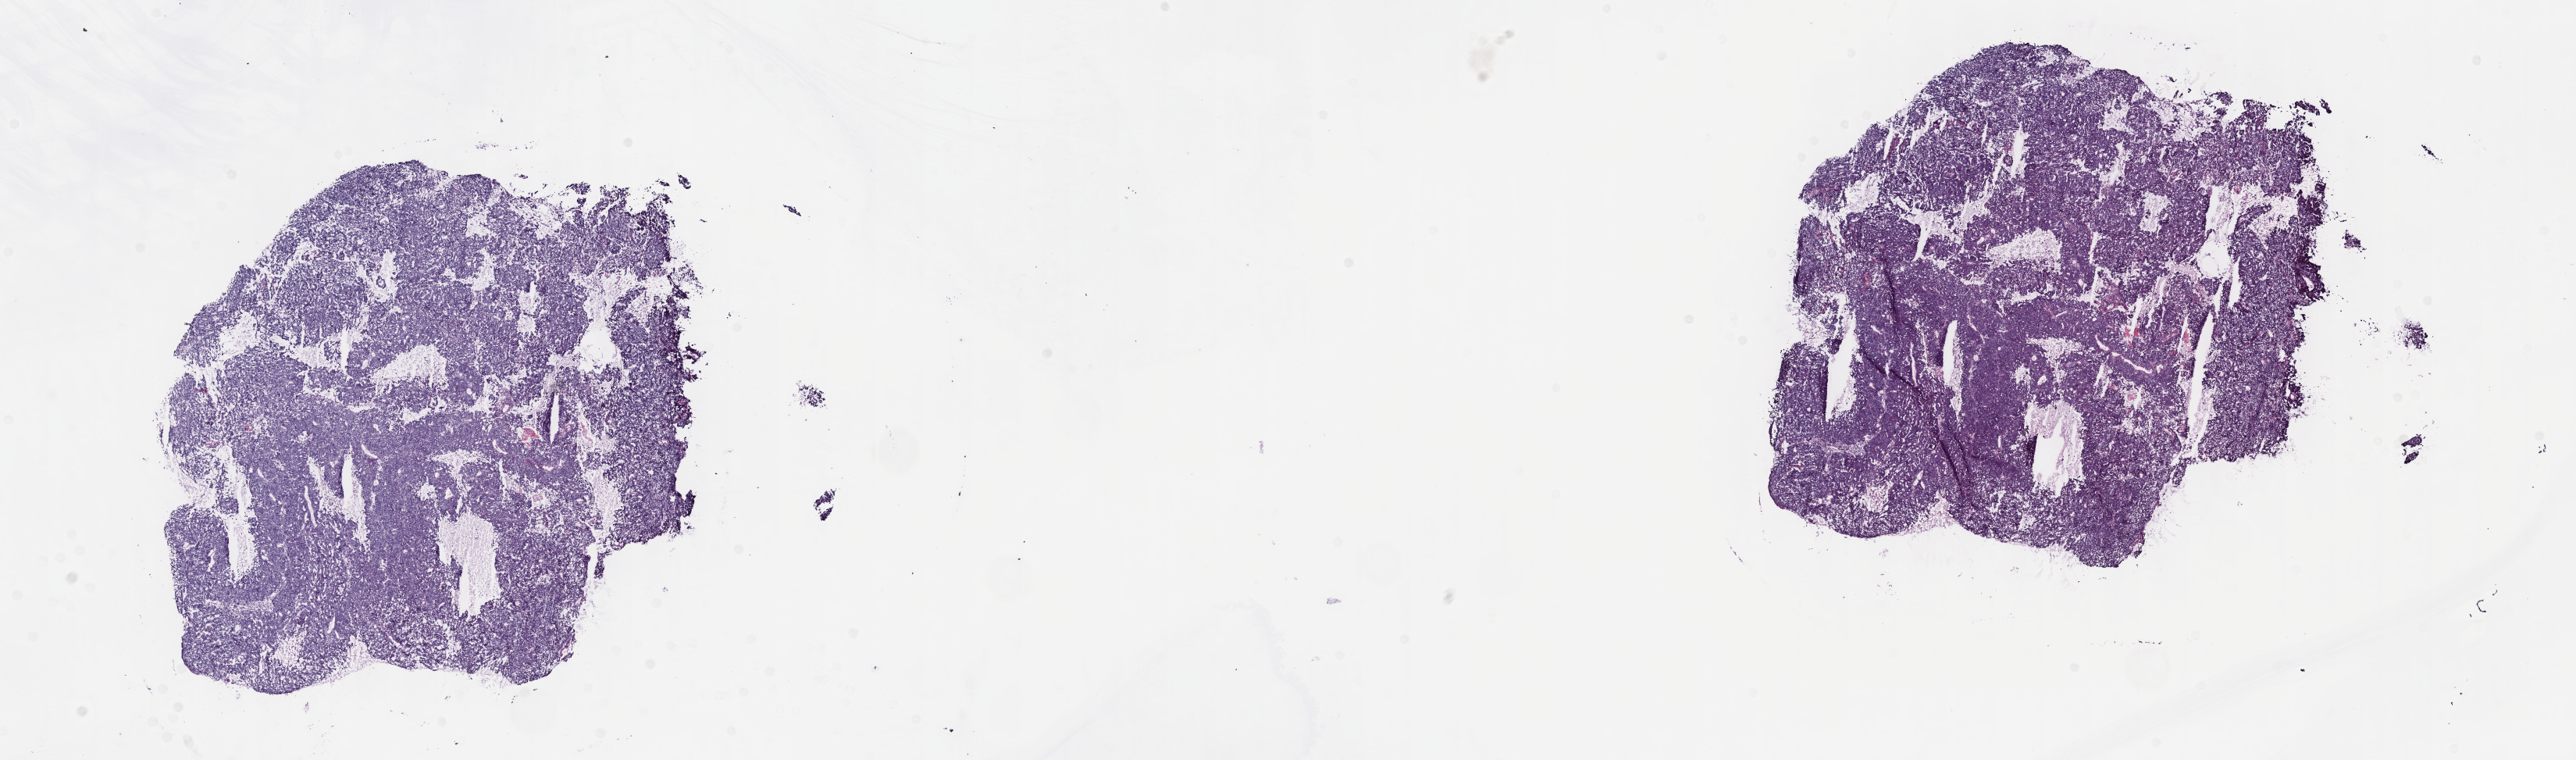
Whole-slide histology image, H&E, shown as a low-resolution overview of the whole scanned area (about 26.7 x 7.9 mm, slide scanned at 40x); frozen section from the top of the tissue portion; sample: primary tumour, cervix. Female patient; age at initial diagnosis 60 years.
Histologic diagnosis: Squamous cell carcinoma, NOS (cervix uteri).